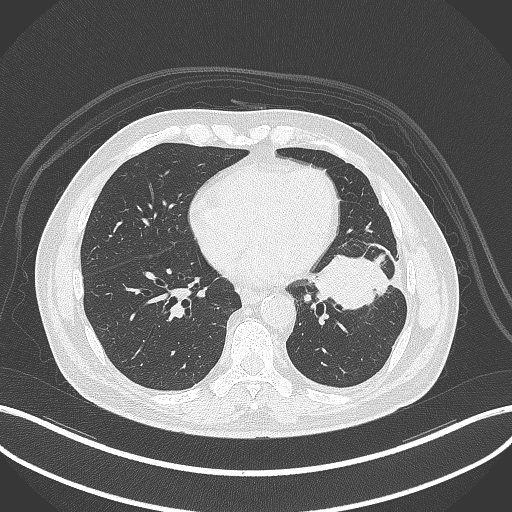
Chest CT, one axial slice; slice 137 of 230 in the series (ordered by position); reconstruction kernel B70f; lung window (W 1500 / L -600 HU); 1 mm slice thickness; 512 × 512 image matrix, field of view 400 × 400 mm. Patient: male, 68 years. Case-level facts recorded for this patient, not image findings: clinical TNM (as recorded): T2b N0 M0.
Annotated regions visible in this slice (rectangle marked by the reading radiologist):
- lung tumour (recorded histology: squamous cell carcinoma): bounding box (x1, y1, x2, y2) in pixels: (313, 252, 391, 313)